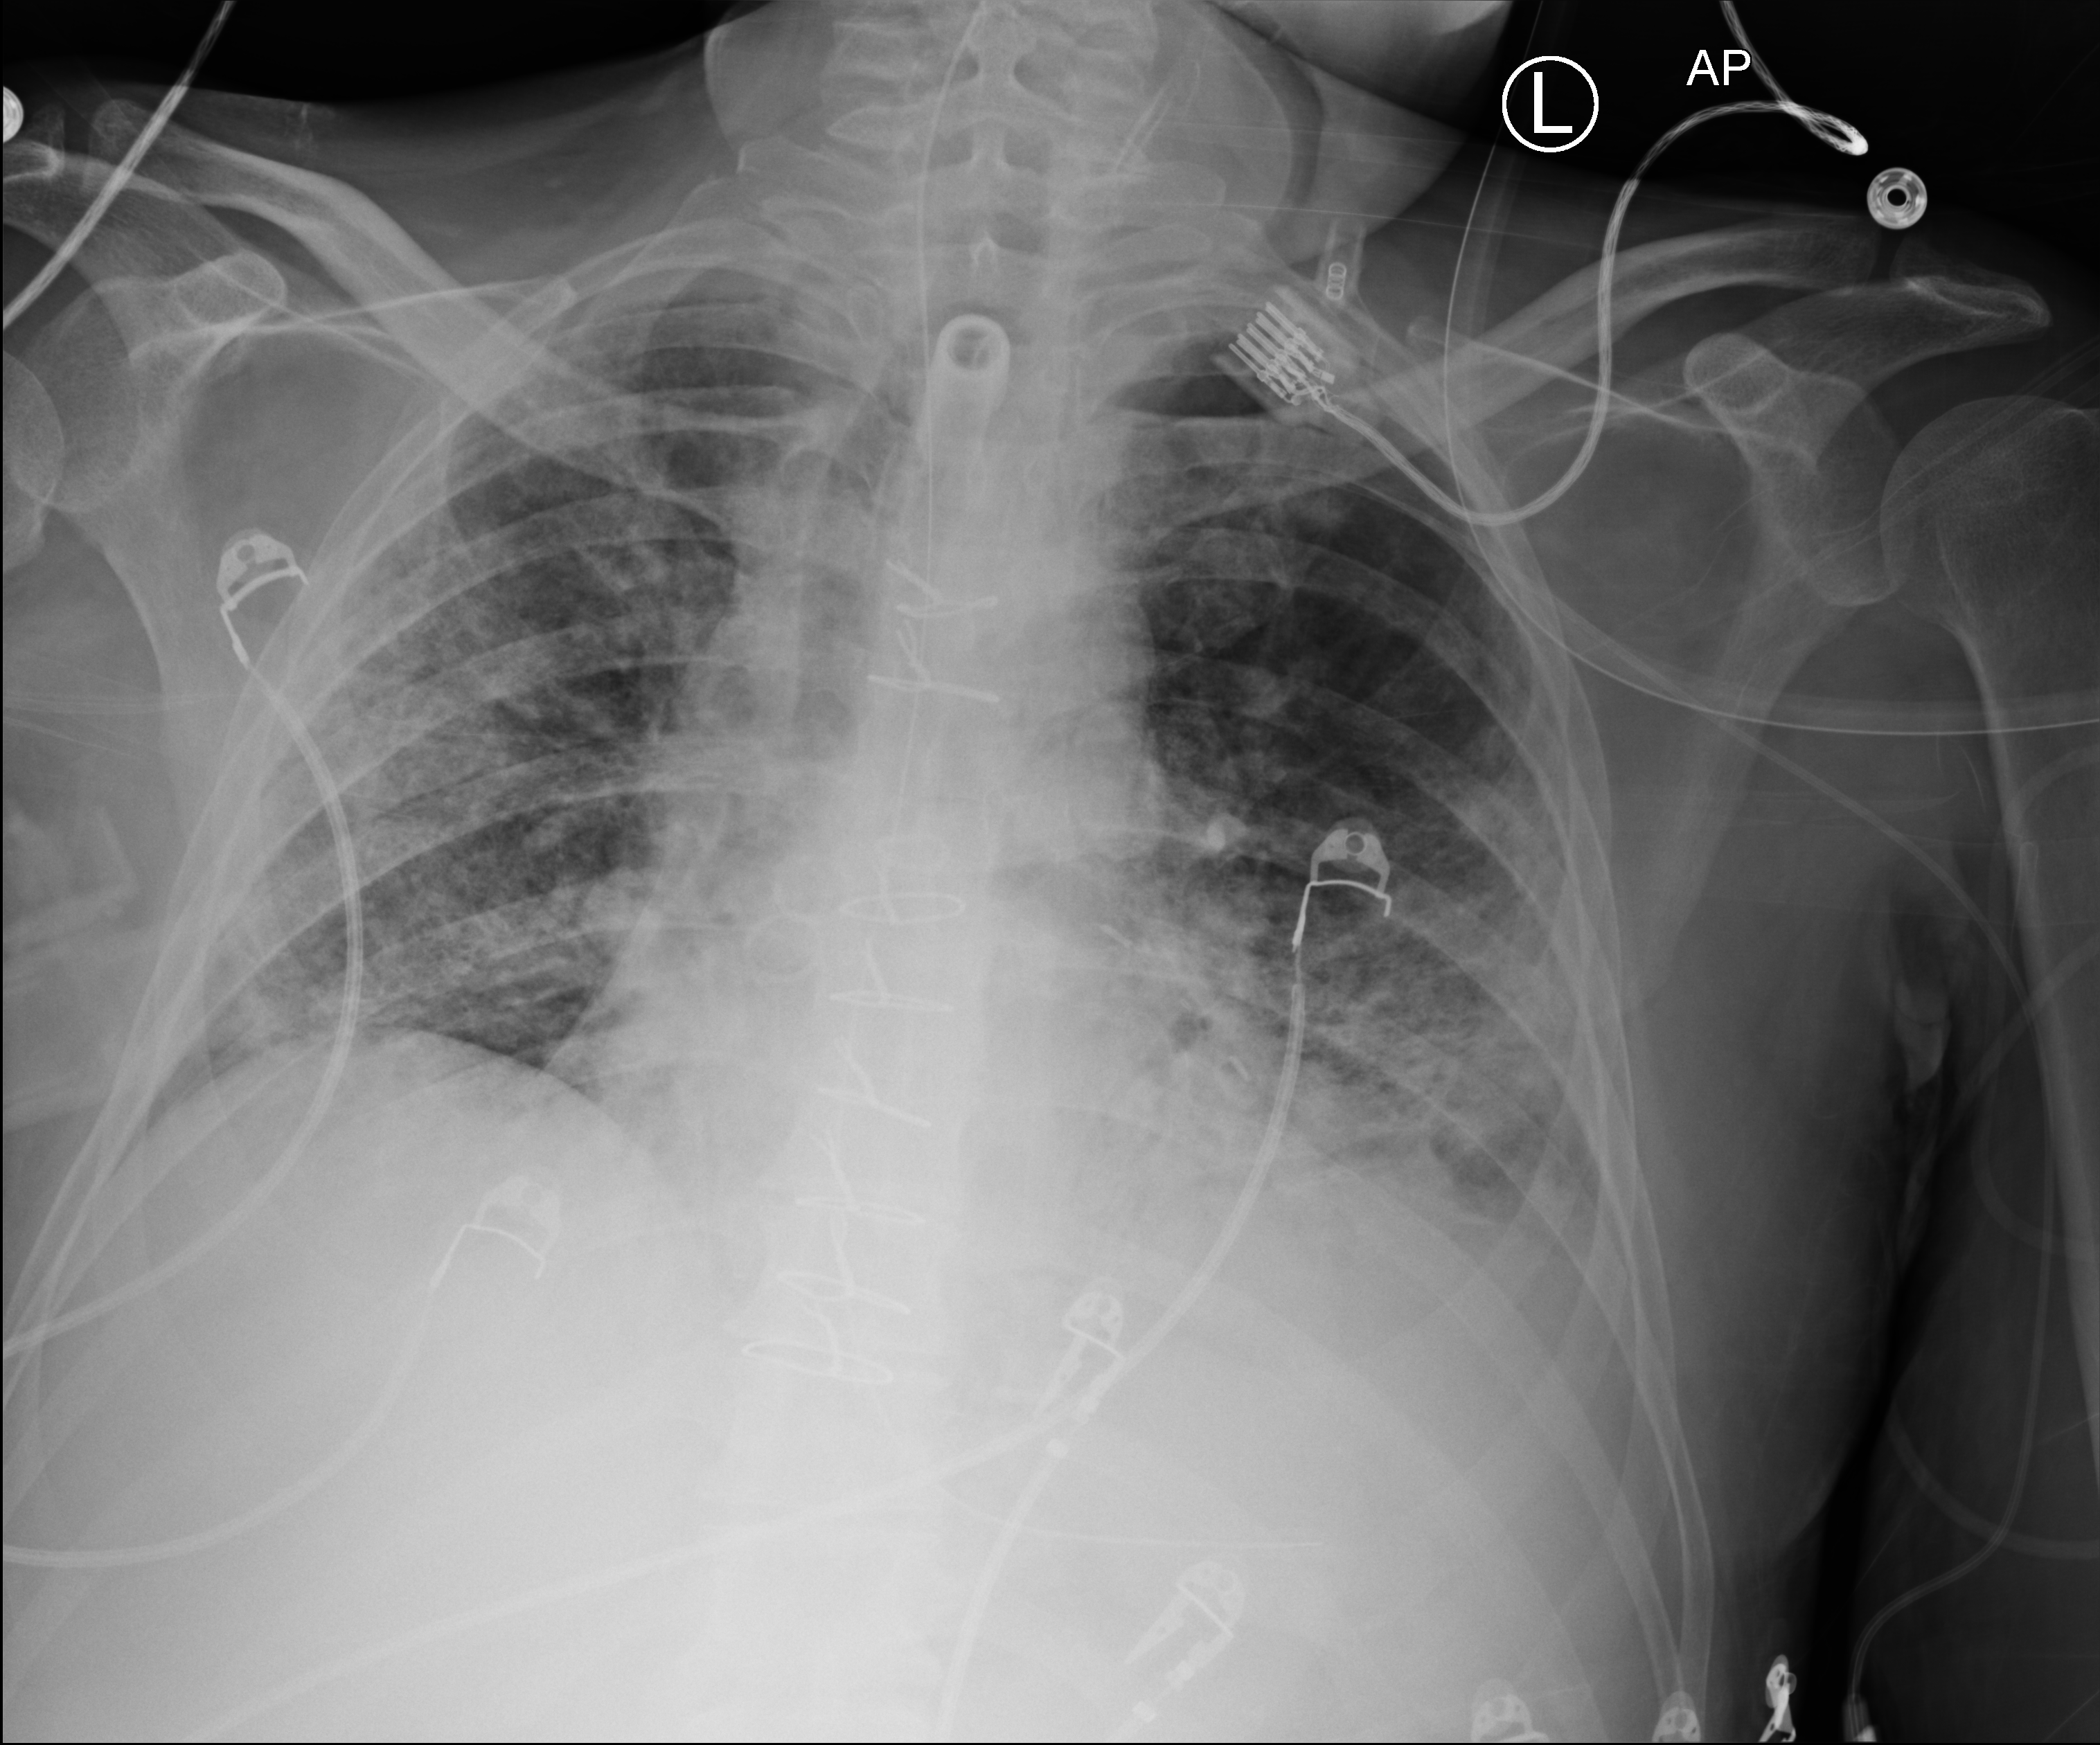
Bedside chest radiograph (computed radiography); anteroposterior (AP) projection. Patient hospitalised with COVID-19; male, aged 18–59 years.
Hospital-stay facts (about this admission, not read from this image; timing relative to this image not recorded): admitted to intensive care during this hospital stay: yes; other chronic lung disease (admission record): yes; mechanically ventilated during this hospital stay: yes.